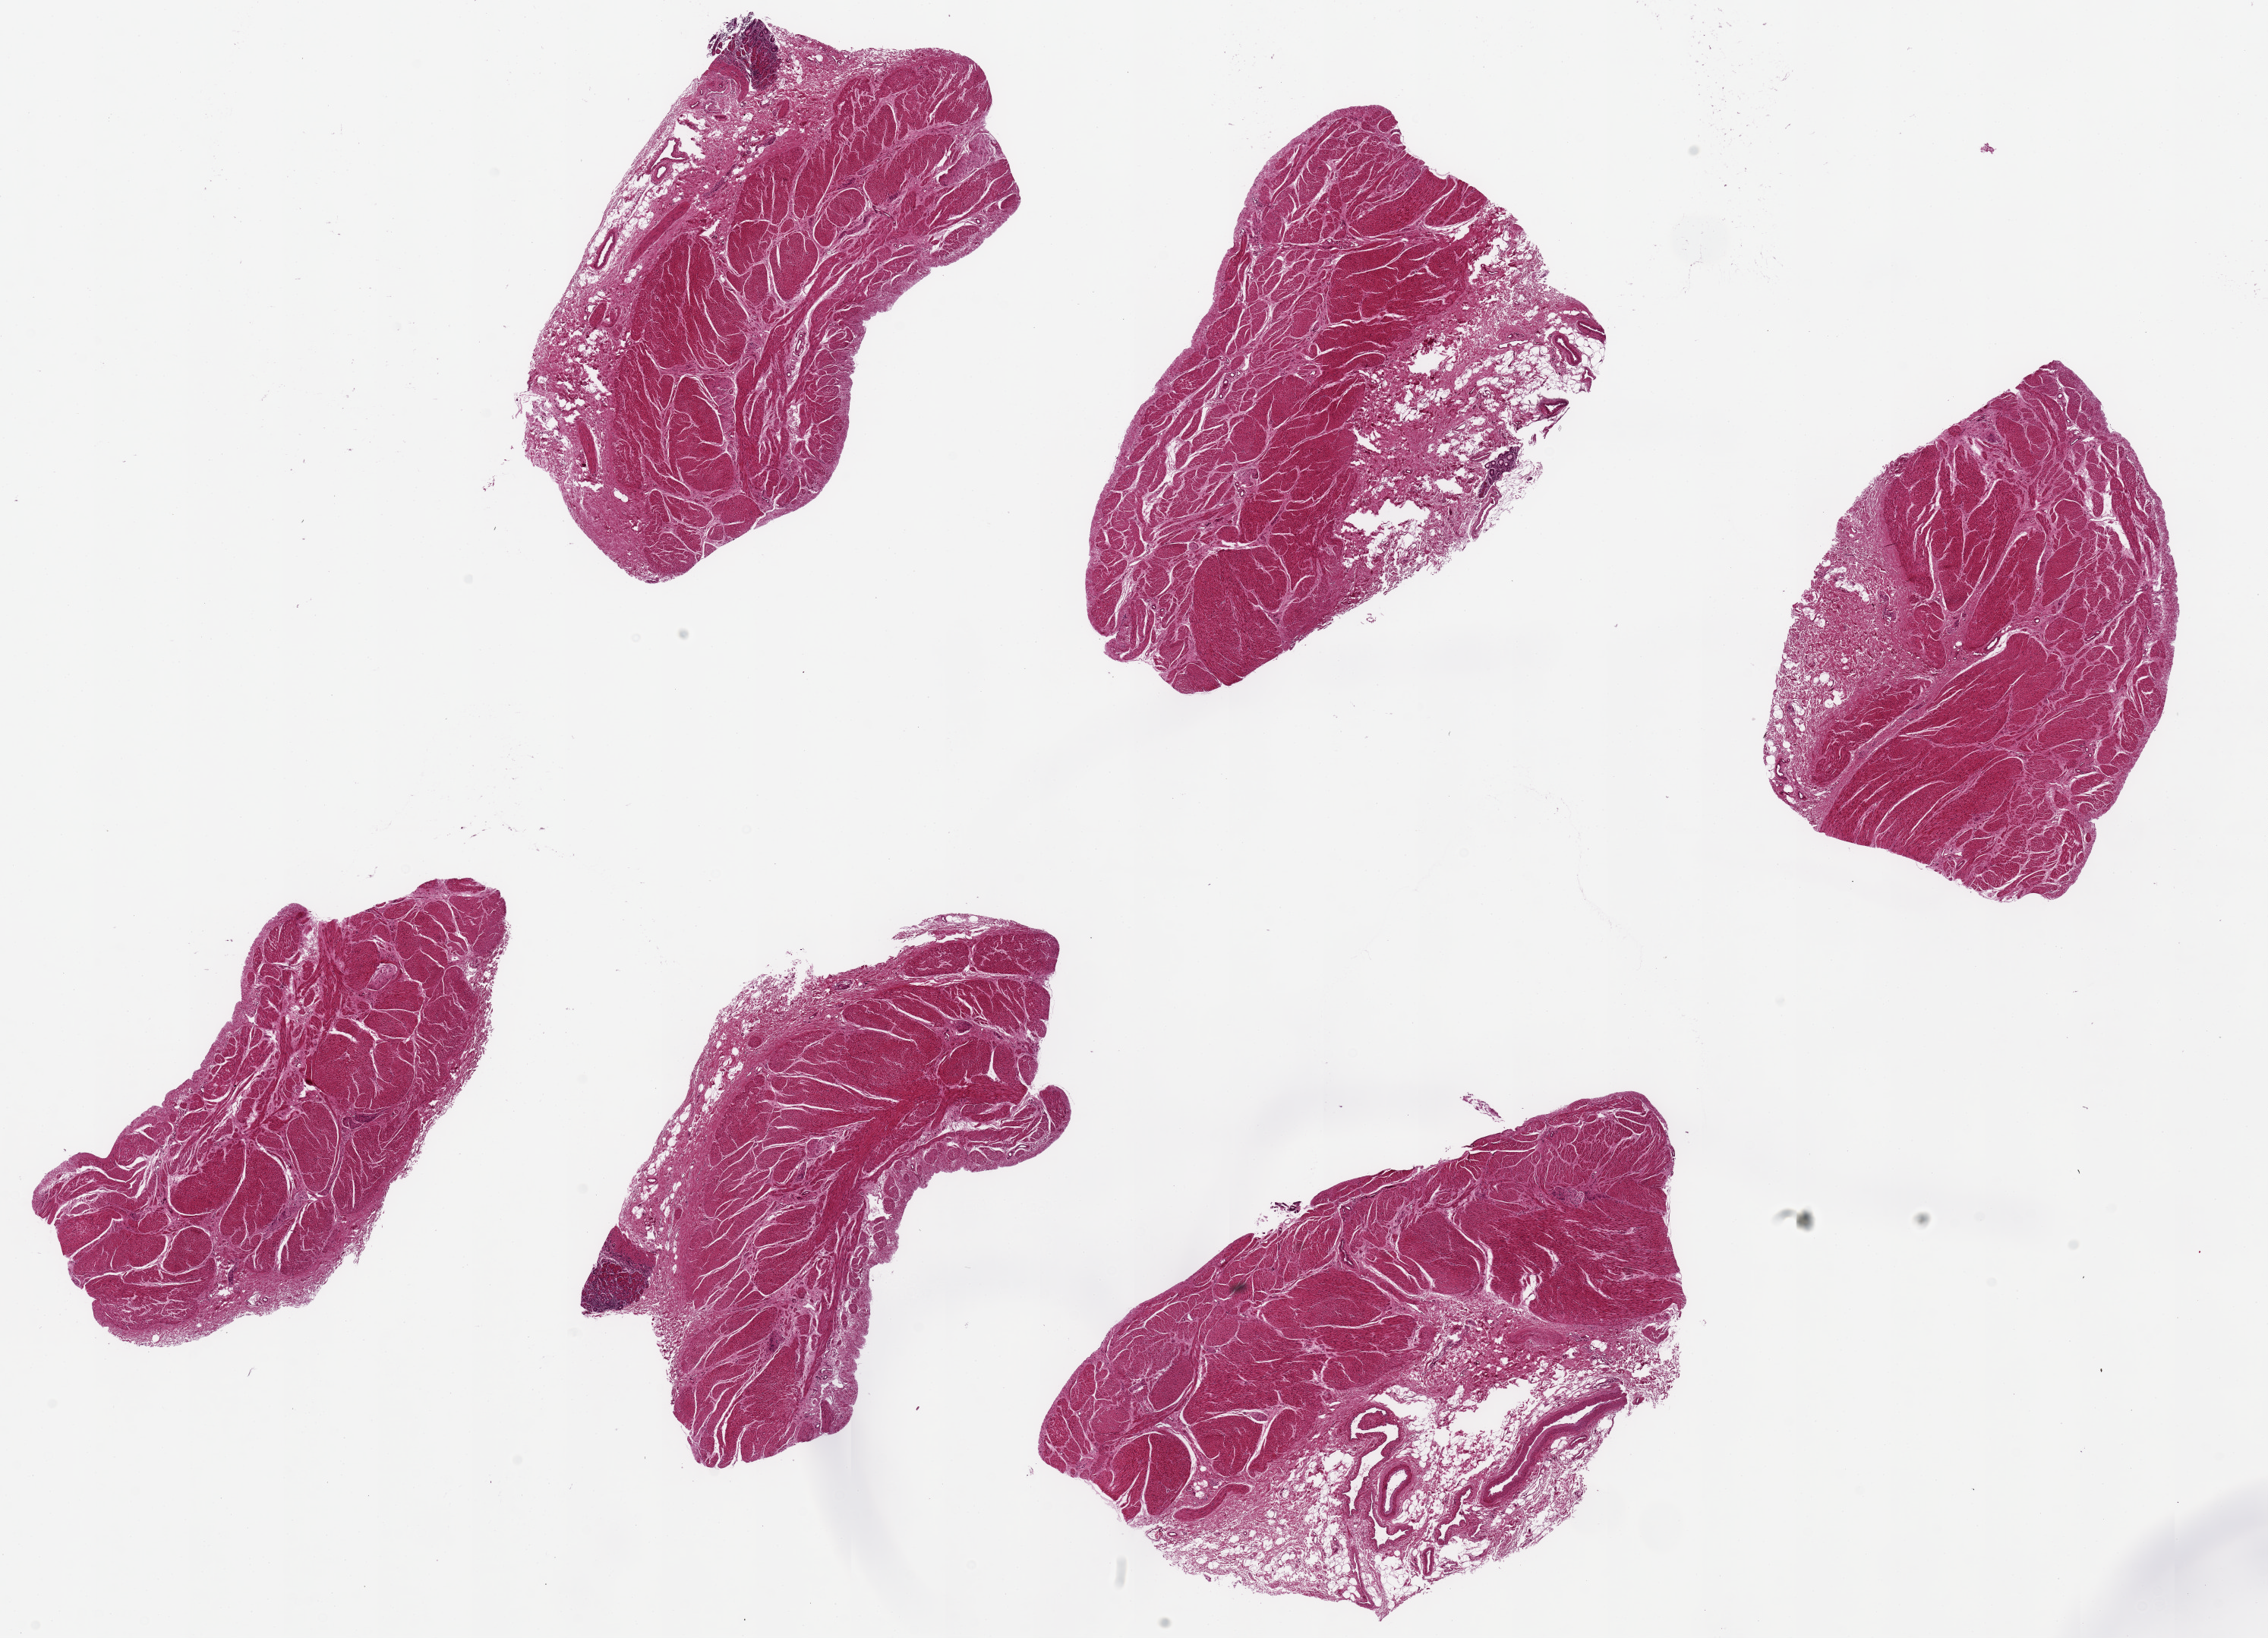
H&E whole-slide image — shown as a low-resolution overview of the whole scanned area (about 23.6 x 17.1 mm); PAXgene-fixed paraffin-embedded (PFPE) section; section of stomach (target tissue); tissue donor sample. Donor: male.
Reviewer comment on this tissue sample: 6 pieces, up to 7x4mm; all pieces contain mostly muscle; only 2 have minute foci of mucosa.